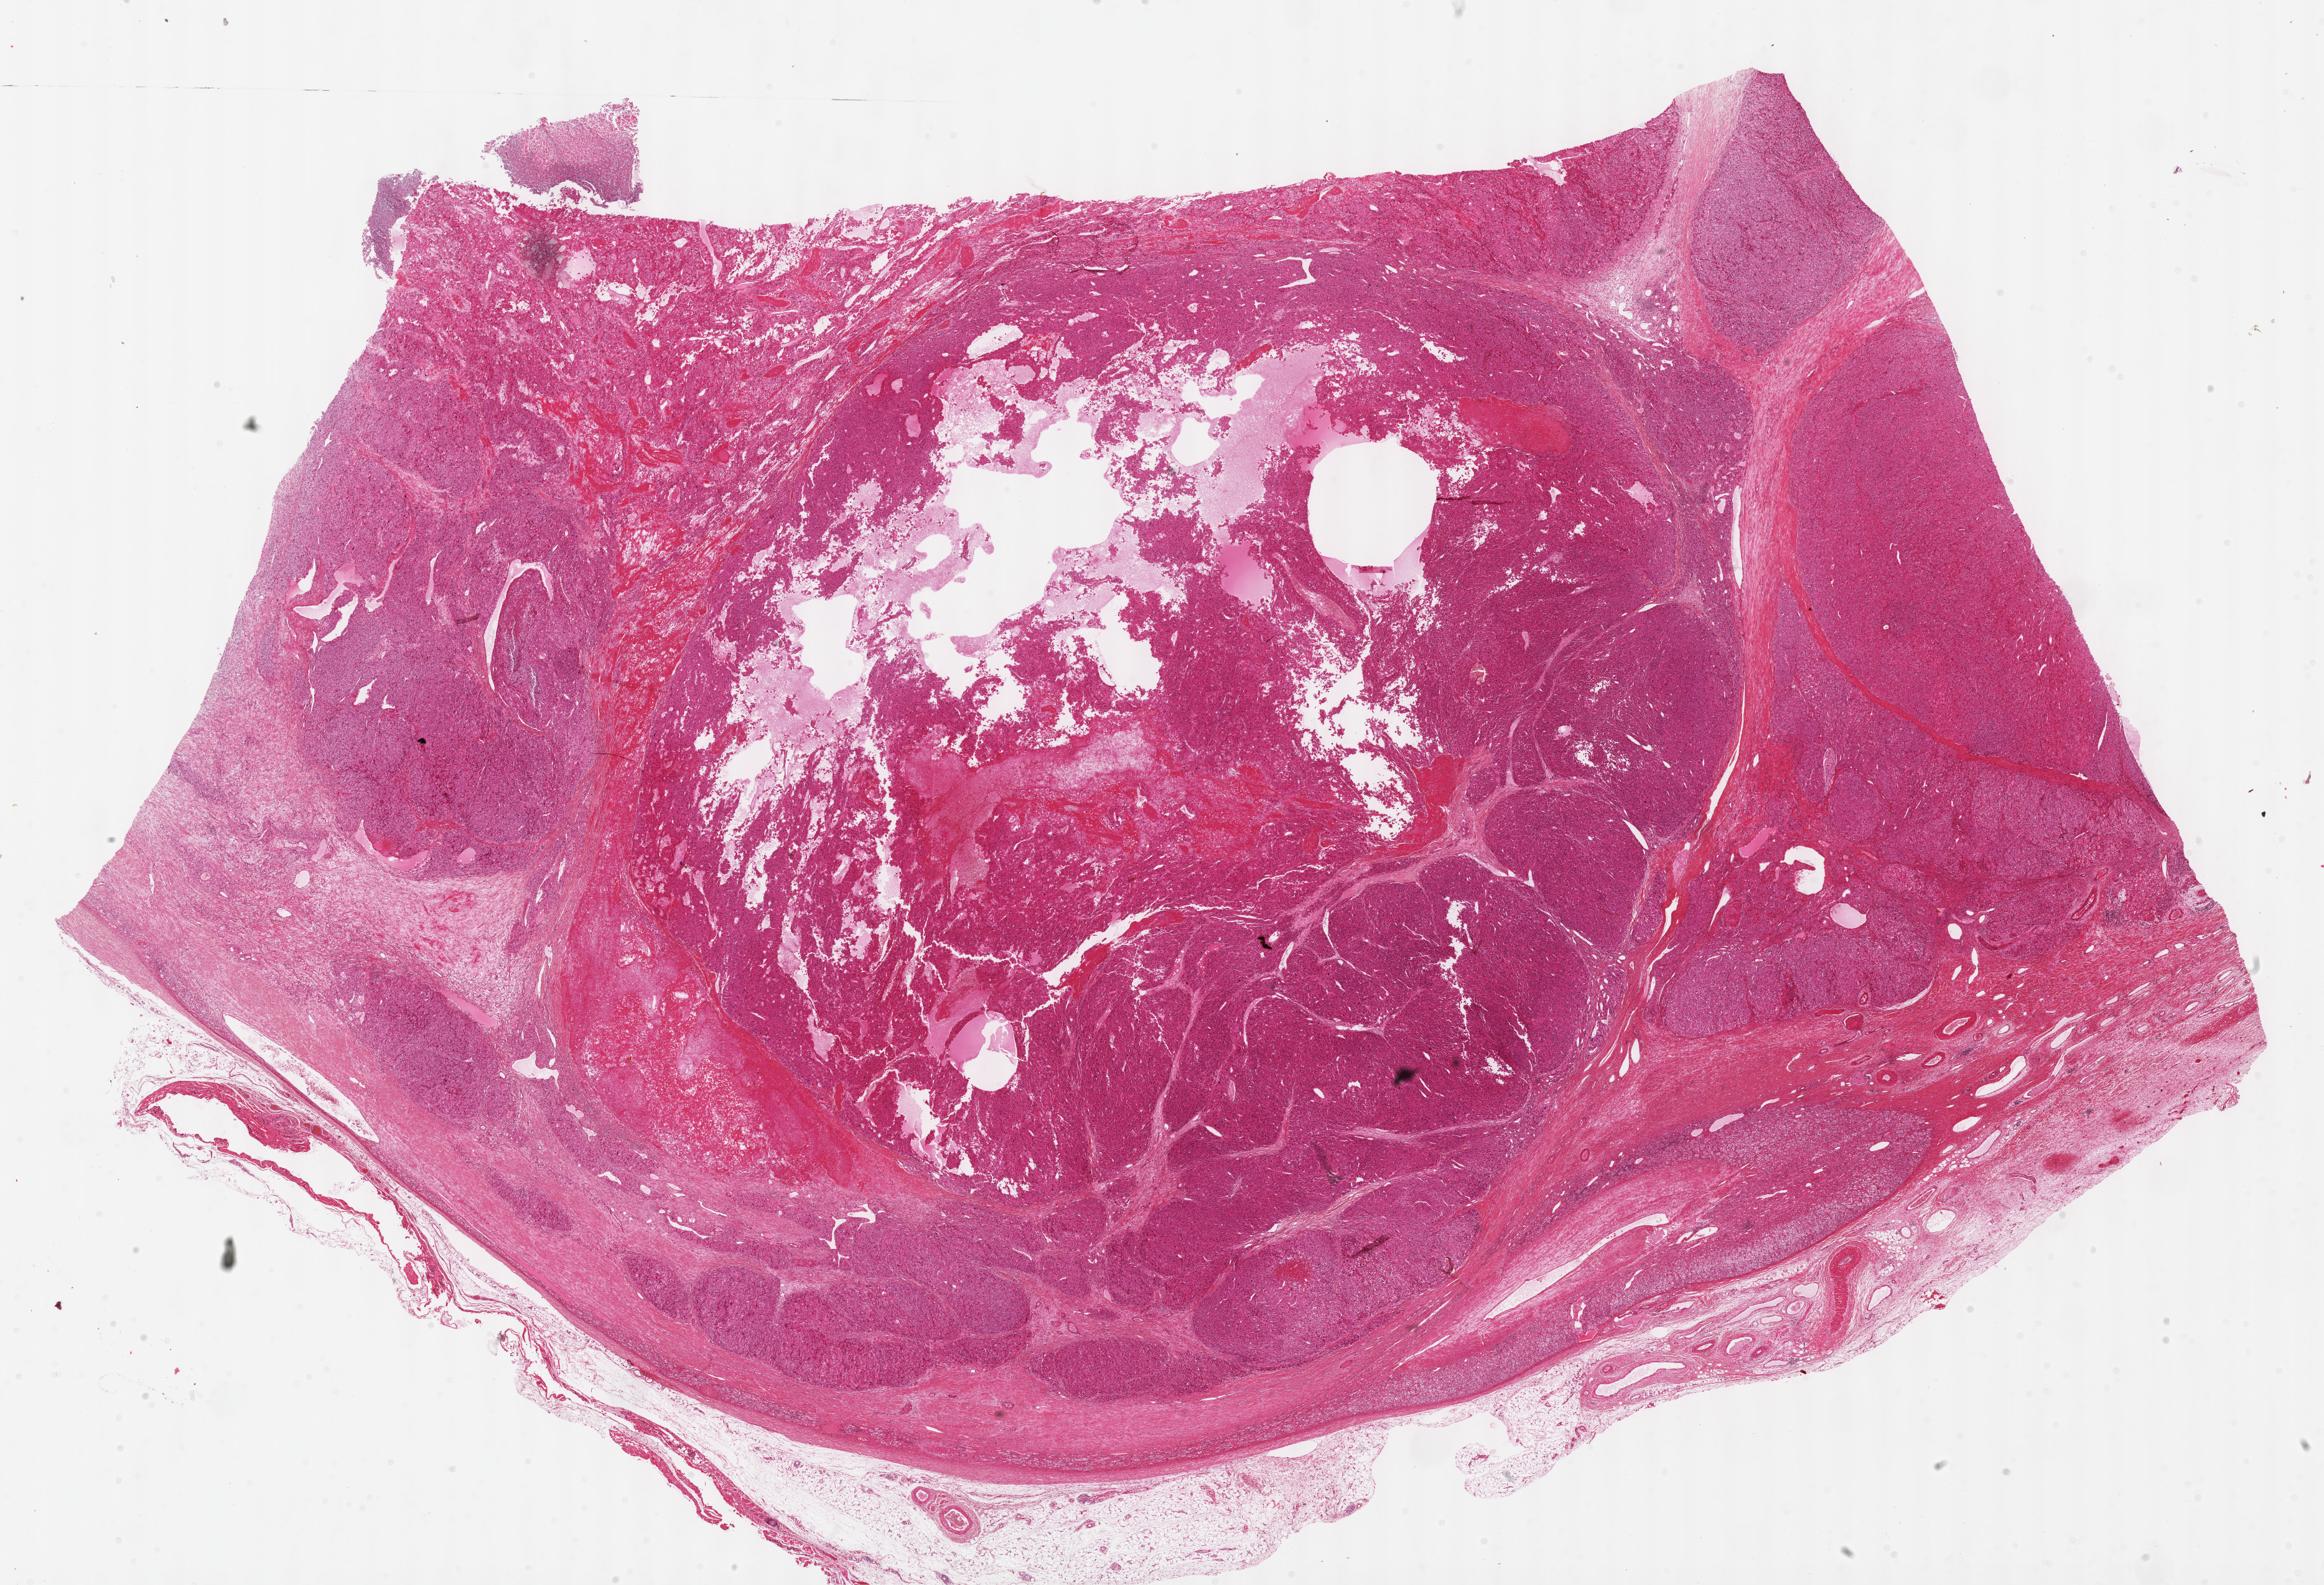
H&E-stained whole-slide image, low-resolution overview of the scanned area, about 30.2 x 20.6 mm, FFPE section, primary tumour sample from the adrenal cortex. Male patient; age at initial diagnosis 23 years.
Pathologic diagnosis: Adrenal cortical carcinoma (cortex of adrenal gland).